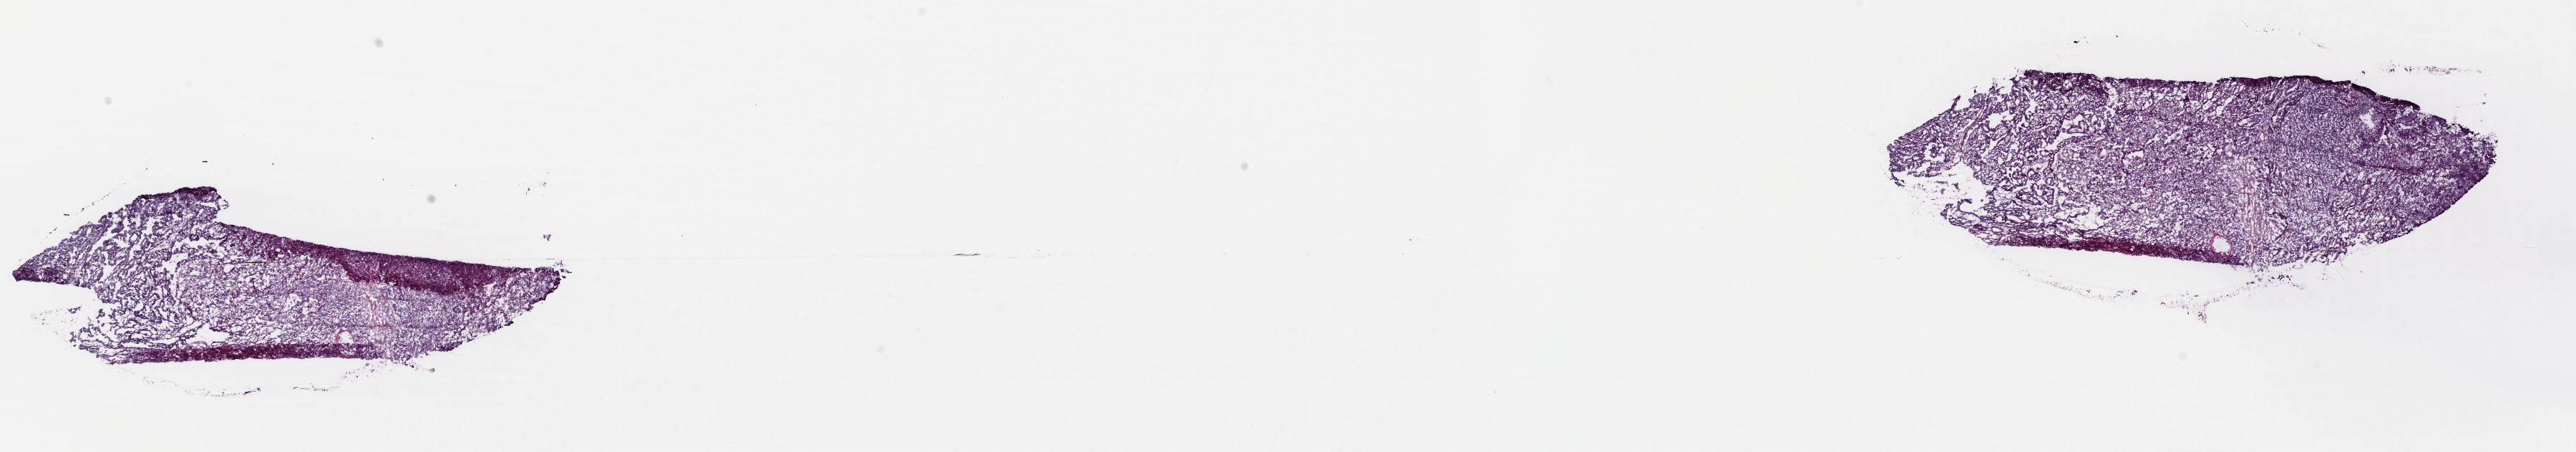
Whole-slide histology image, H&E-stained — low-resolution overview of the scanned area, about 28.4 x 5.0 mm (from a 40x scan); frozen section; primary tumour sample from the uterus. Patient: female, age at initial diagnosis 68 years. Histologic grade: G3 (poorly differentiated). Pathologist review of this section (percent, as recorded): tumour cells 80%, tumour nuclei 90%, normal cells 0%, stromal cells 10%, necrosis 10%. Infiltration values recorded for this section: lymphocyte infiltration 5%, monocyte infiltration 5%, neutrophil infiltration 15%.
Diagnosis: Serous cystadenocarcinoma, NOS (endometrium). FIGO stage: II.